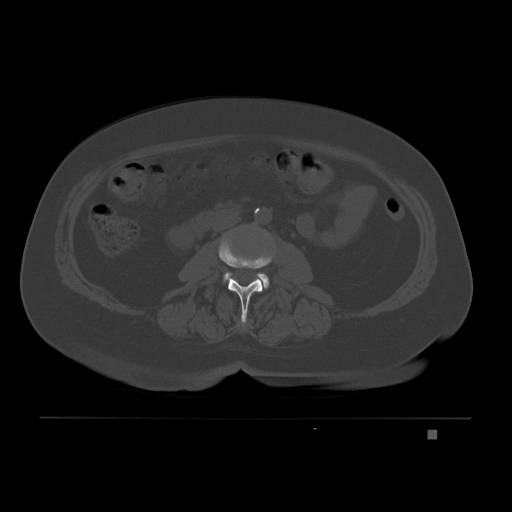
CT including the spine, one axial slice; slice 58 of 221 in the series (ordered by position); bone window (W 1800 / L 400 HU); 512 × 512 image matrix, field of view 474 × 474 mm. Female patient, age 63 years. Case-level facts recorded for this patient, not image findings: primary cancer: breast.
Annotated regions visible in this slice (semi-automatic segmentation, software-assisted and operator-edited):
- L2 vertebra: bounding box <218,238,273,324> (left, top, right, bottom; pixels)
- L3 vertebra: <223,272,269,289>